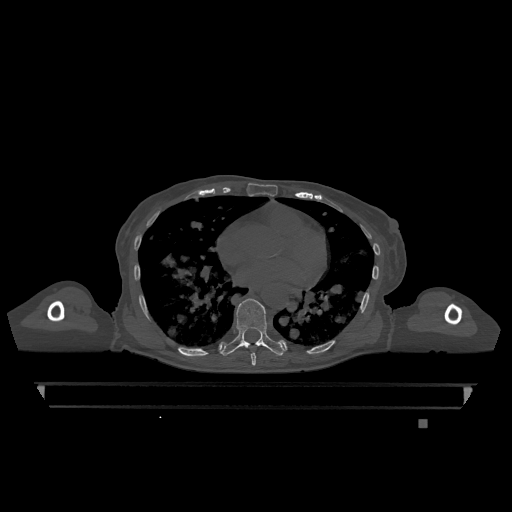
CT including the spine, one axial slice; position 701 of 1317 along the scan axis; bone window (W 1800 / L 400 HU); 0.5 mm slice thickness; 512 × 512 image matrix, field of view 500 × 500 mm. Patient: female, 74 years. From the clinical record (not read from this slice): primary cancer: lung.
Outlined on this slice (semi-automatic segmentation, software-assisted and operator-edited):
- T7 vertebra: bounding box (x1, y1, x2, y2) in pixels: (251, 353, 256, 366)
- T9 vertebra: (221, 298, 284, 356)